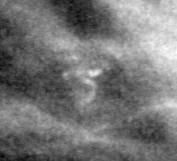
Crop from a digitized film mammogram around one marked abnormality; right breast; MLO view; BI-RADS breast density category 3 (scale 1–4).
Calcifications, morphology pleomorphic, distribution clustered; BI-RADS assessment category 4; subtlety rating 2 on a 1 (subtle) to 5 (obvious) scale; pathology (as recorded): benign.